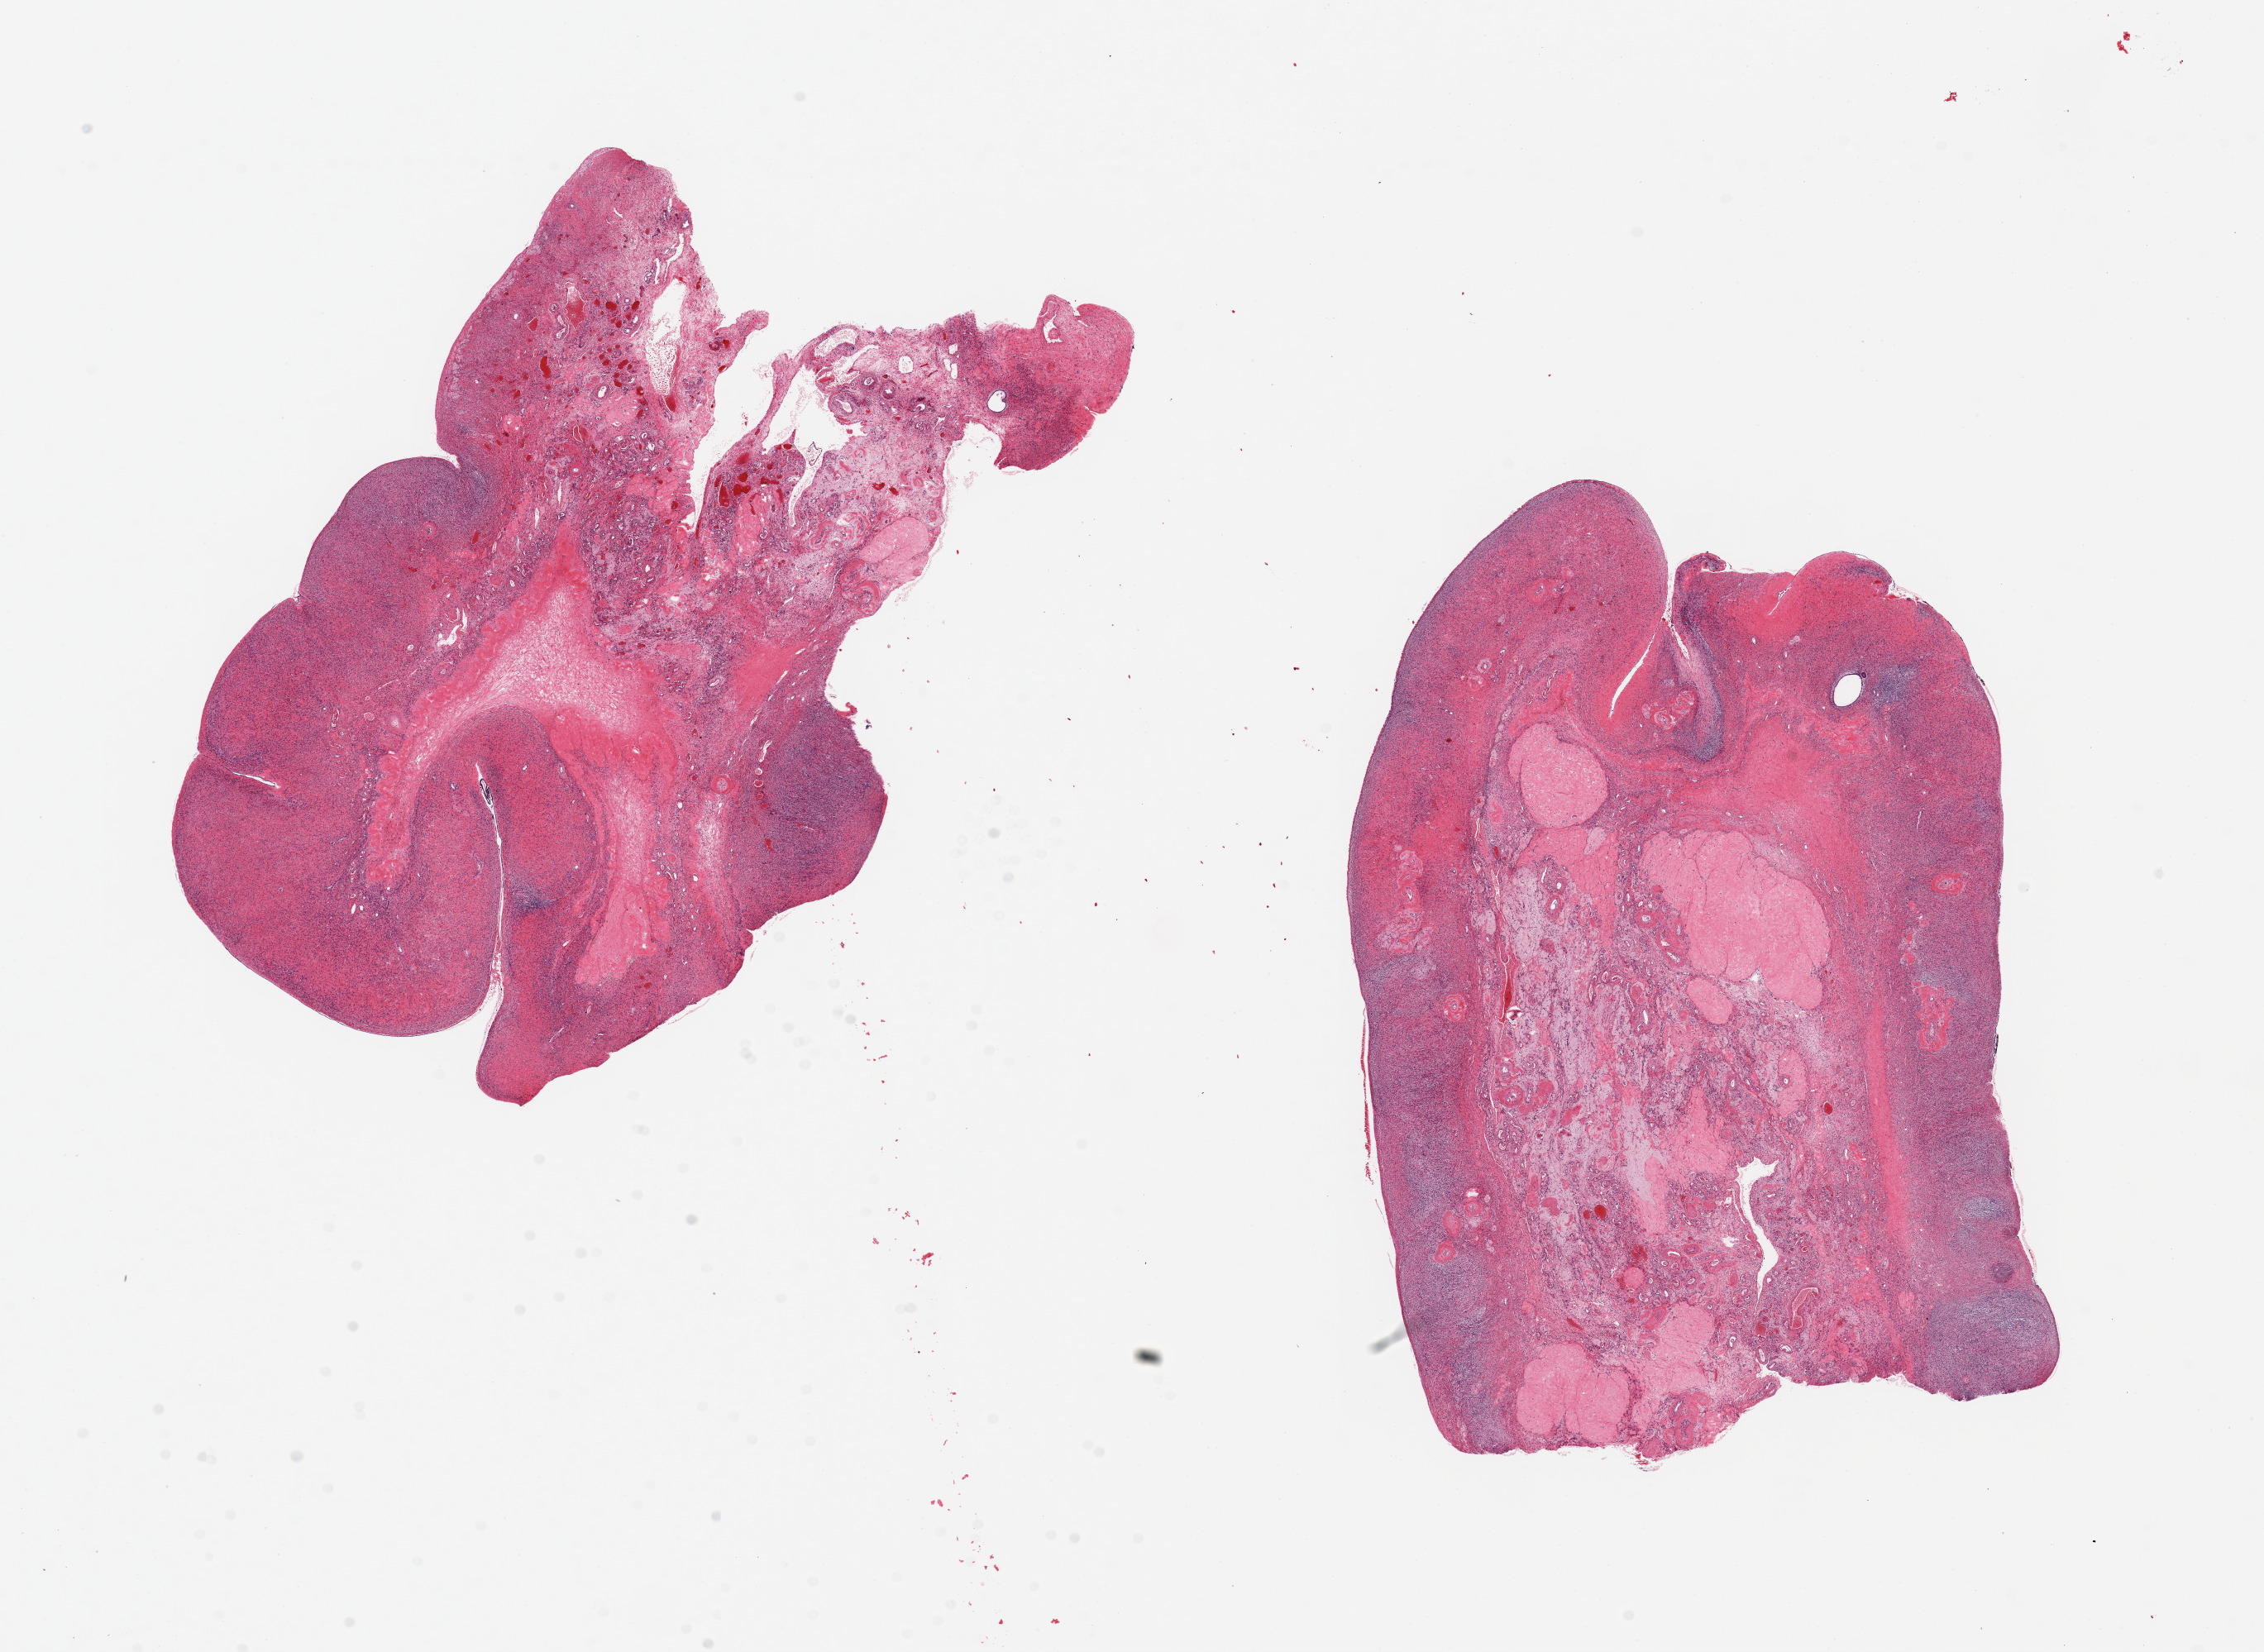
Digitized H&E-stained section — low-resolution overview of the scanned area, about 21.7 x 15.8 mm; PAXgene-fixed, paraffin-embedded tissue; sampled site (target tissue): ovary; donor tissue sample.
Pathologist's review note for this sample: 2 pieces ~8x6mm. Post menopausal atrophy, prominent corpora albicantia.